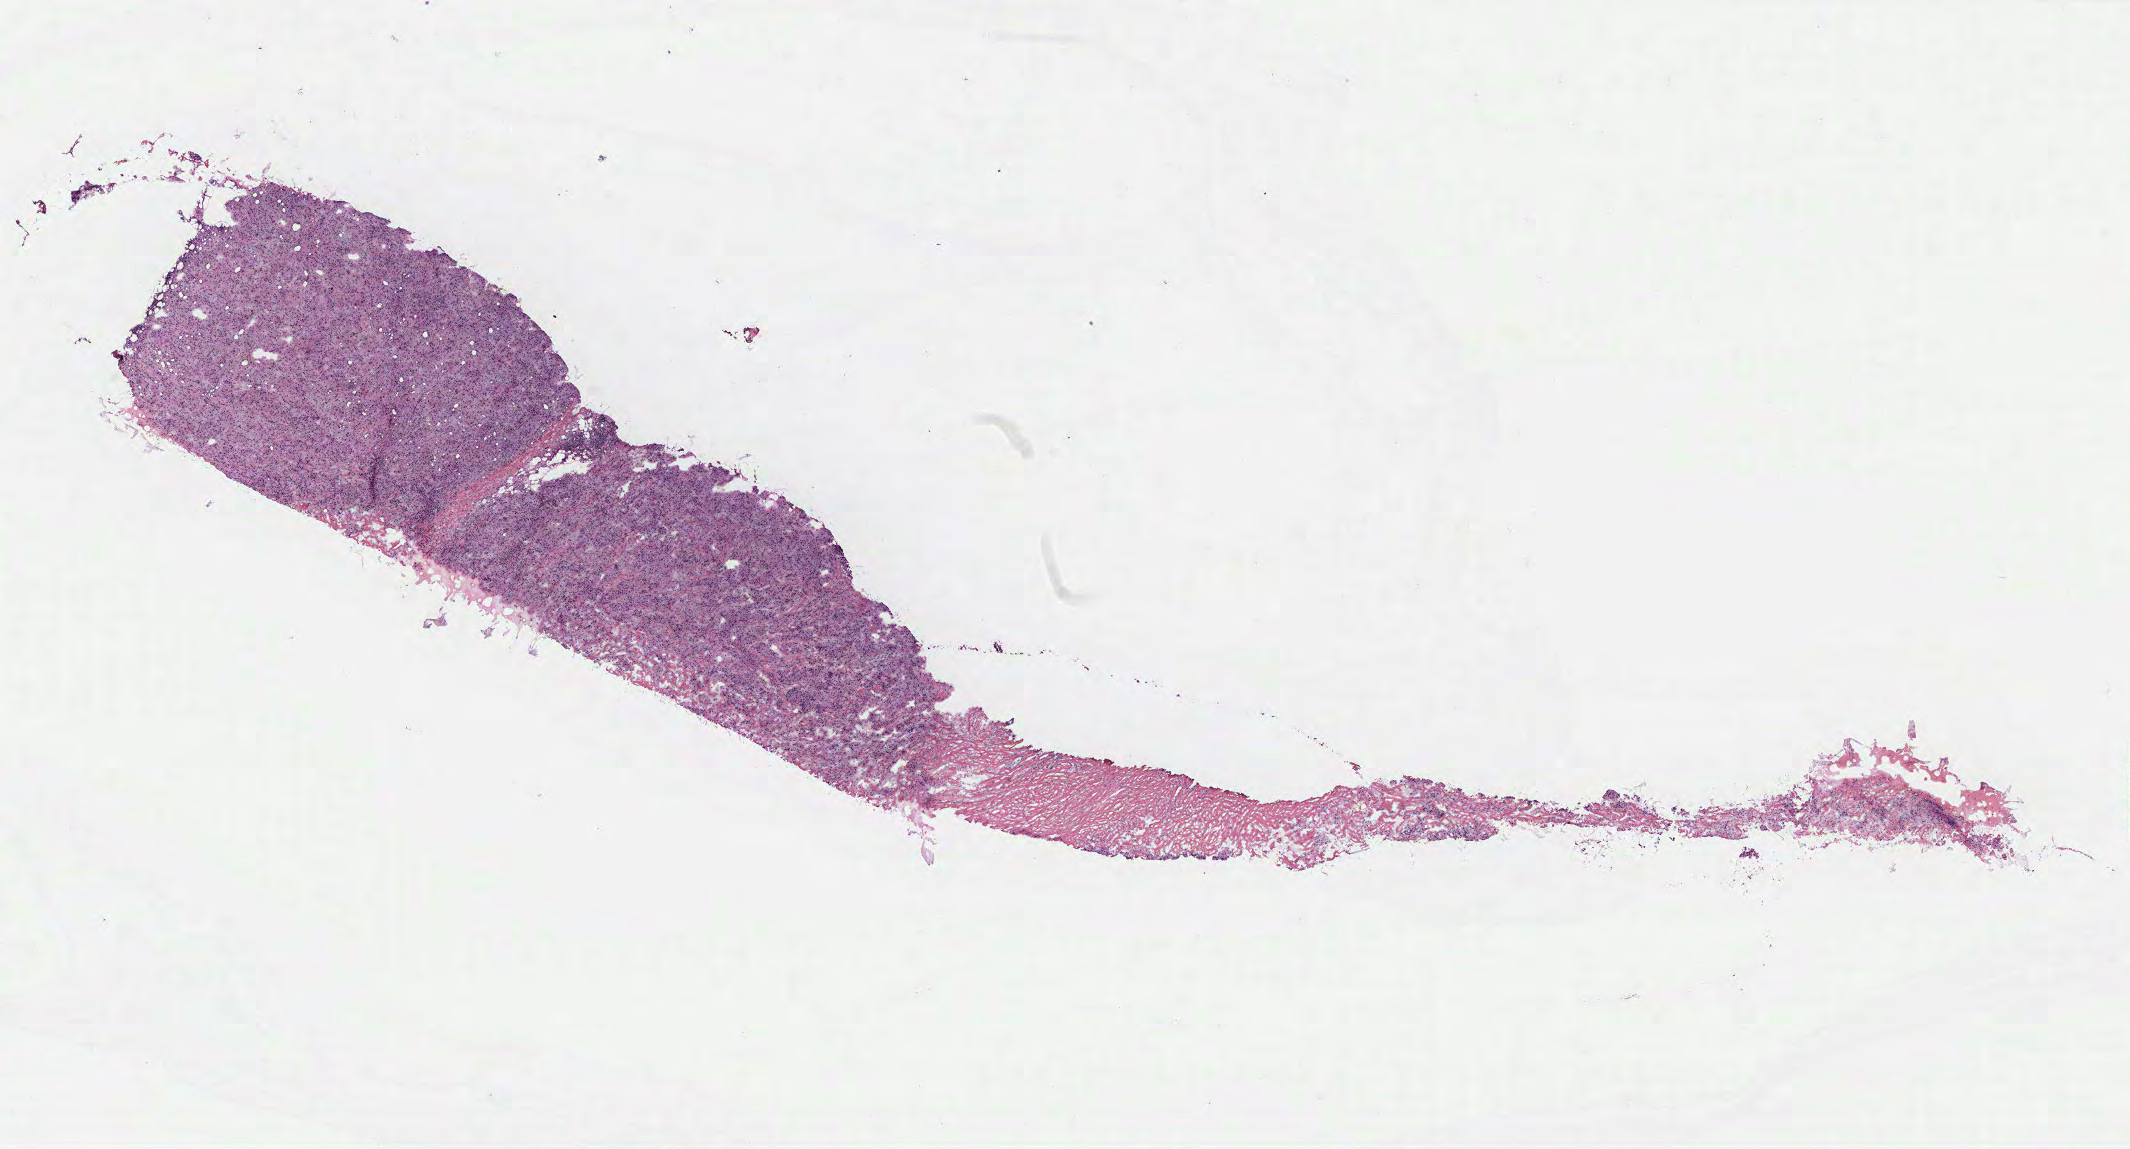
H&E-stained whole-slide image — low-resolution overview of the scanned area, about 17.0 x 9.2 mm (from a 40x scan). 65-year-old female patient.
Specimen: tumour tissue sample, breast.